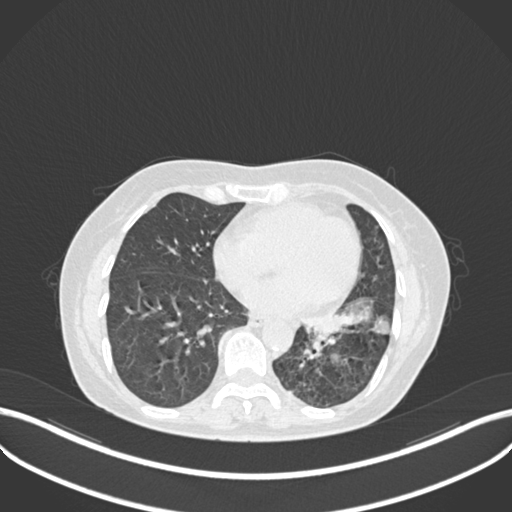
Chest CT, one axial slice. Position 100 of 270 along the scan axis. 120 kVp. Lung window (W 1500 / L -600 HU). 1 mm slice thickness. 512 × 512 image matrix, field of view 400 × 400 mm. Patient: female, 63 years. From the clinical record (not read from this slice): clinical TNM (as recorded): T1b N0 M0.
Structures marked on this image (rectangle marked by the reading radiologist):
- lung tumour (recorded histology: adenocarcinoma): bounding box (x1, y1, x2, y2) in pixels: (296, 302, 392, 341)